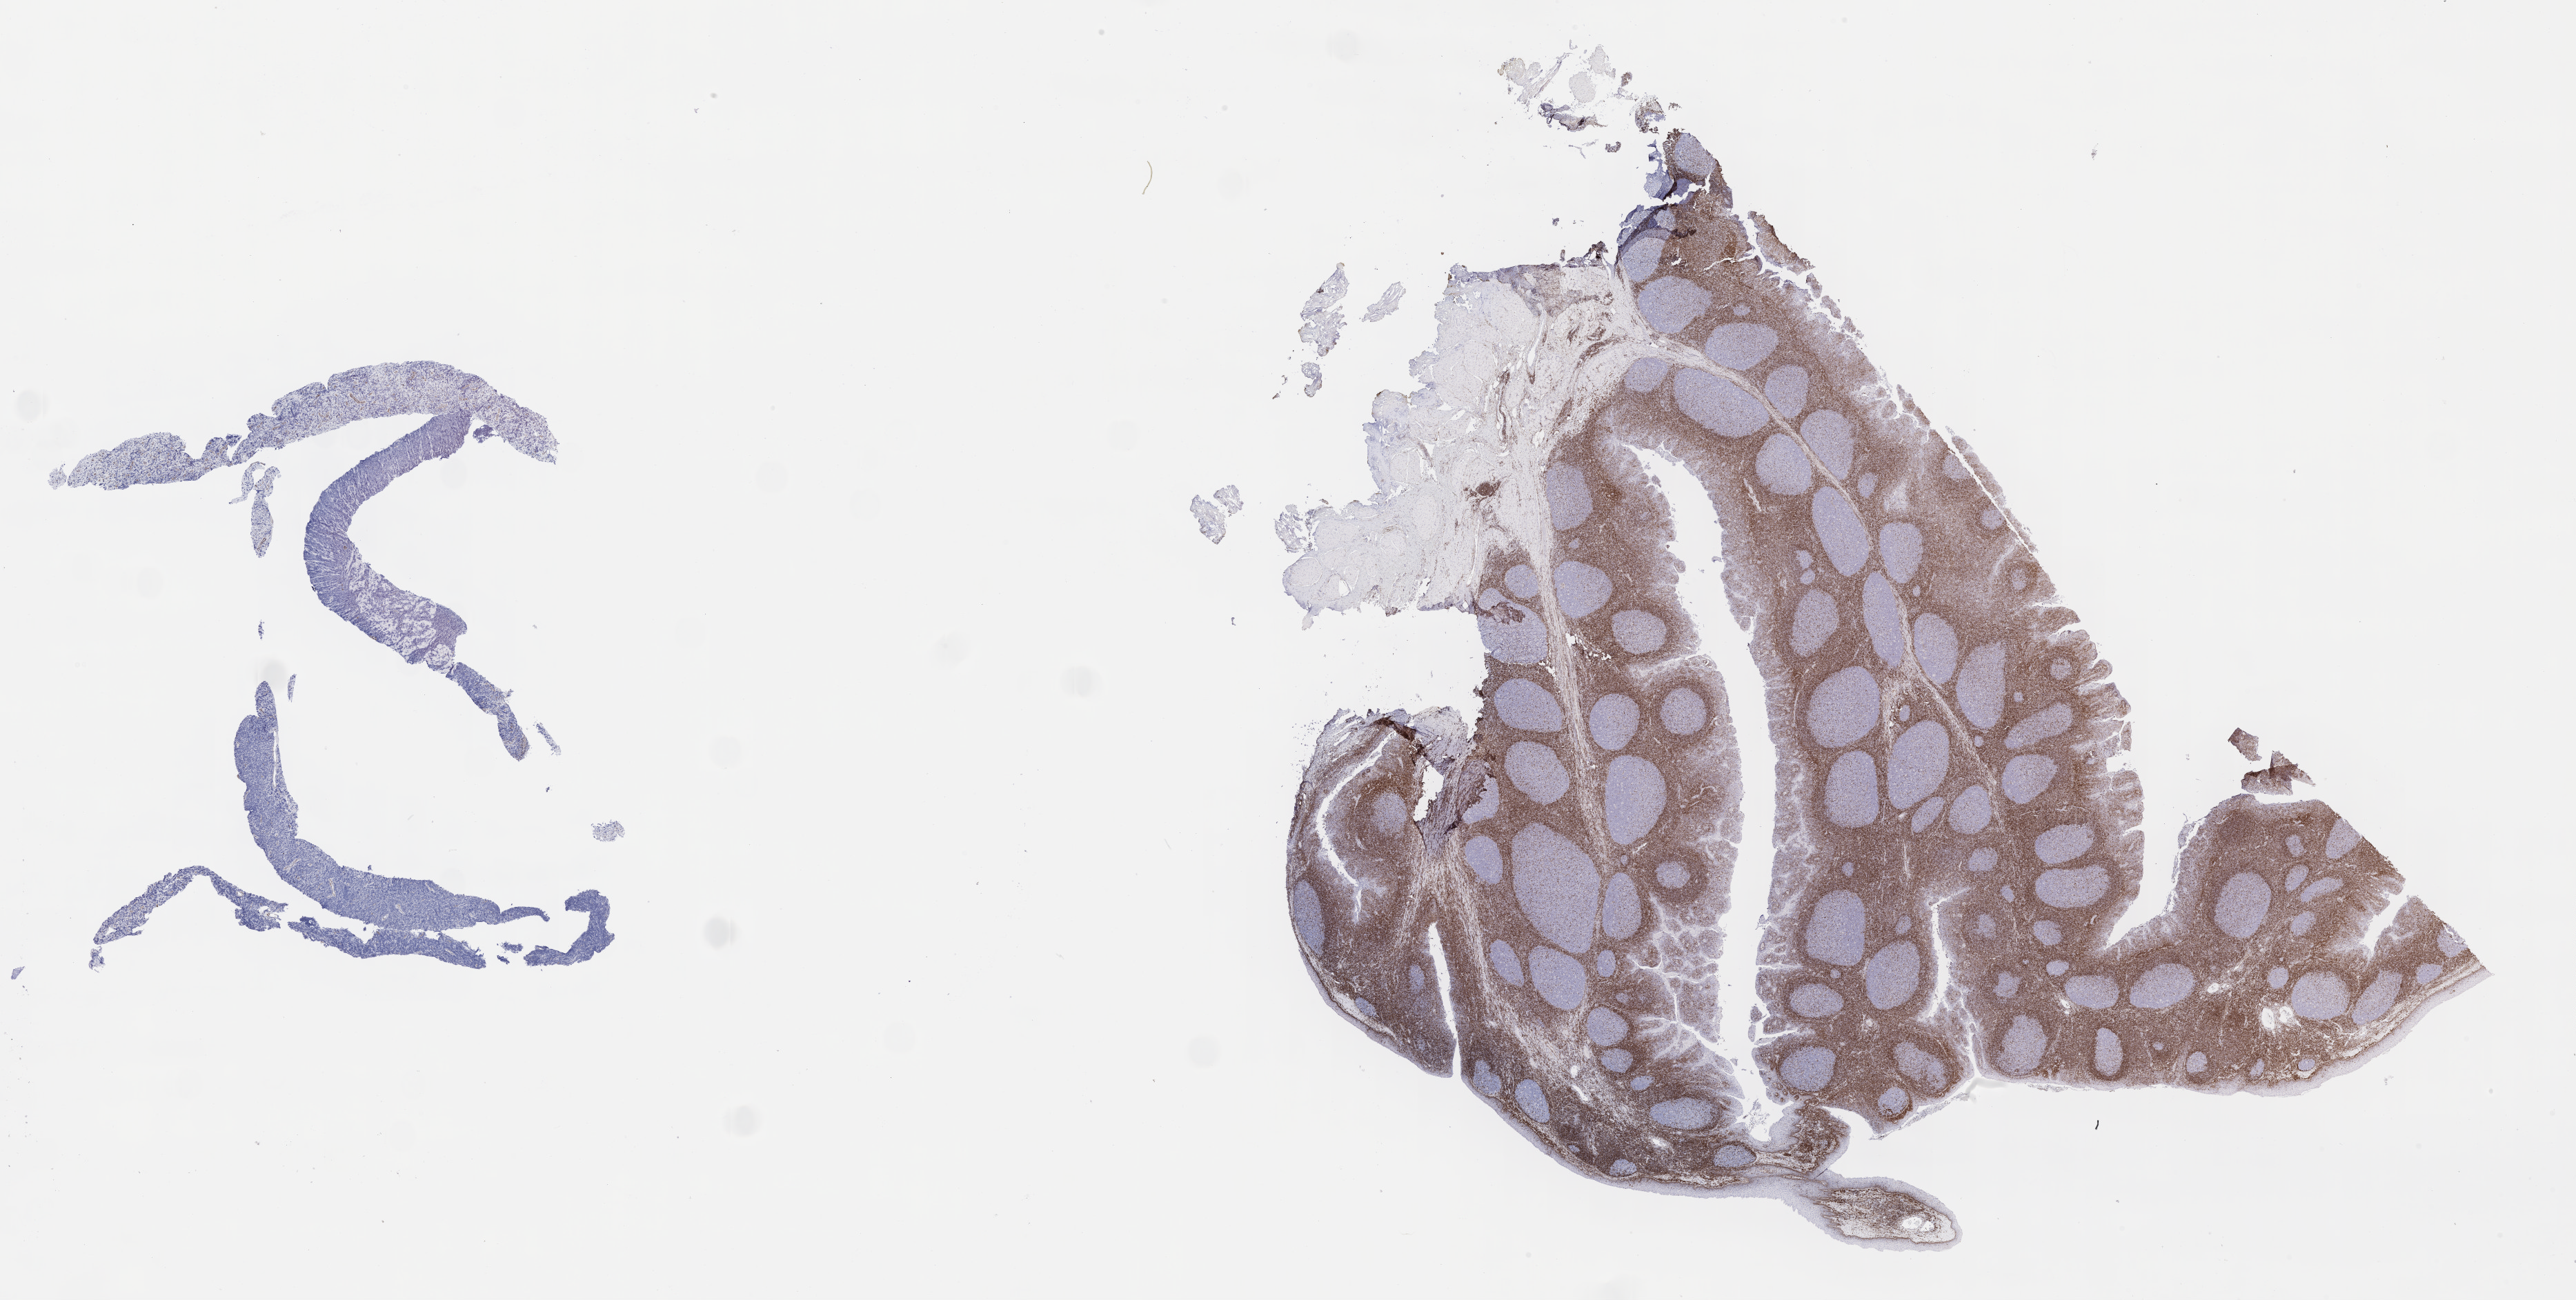
Immunohistochemistry (IHC) whole-slide image stained for BCL2 — a low-resolution overview of the entire scanned area, about 30.2 x 15.2 mm. Specimen: tumor tissue. Site: pleura. Patient: male, age at initial diagnosis 2 years.
Diagnosis: Diffuse large B-cell lymphoma, NOS.